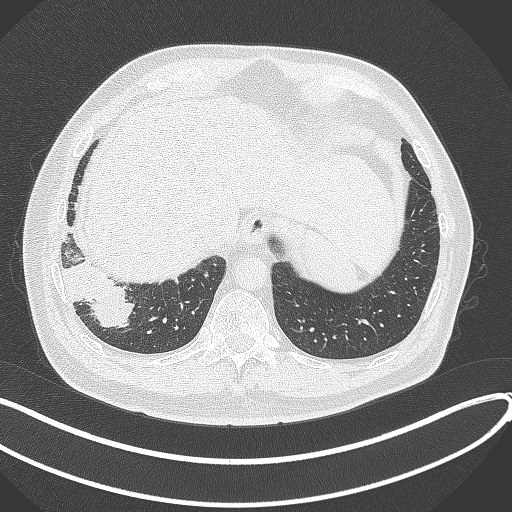
Chest CT, one axial slice. Slice 62 of 360 in the series (ordered by position). Reconstruction kernel B70f. Lung window (W 1500 / L -600 HU). 1 mm slice thickness. 512 × 512 image matrix. Male patient, age 59 years.
Annotated regions visible in this slice (rectangle marked by the reading radiologist):
- lung tumour (recorded histology: adenocarcinoma): bounding box (x1, y1, x2, y2) in pixels: (62, 254, 132, 334)